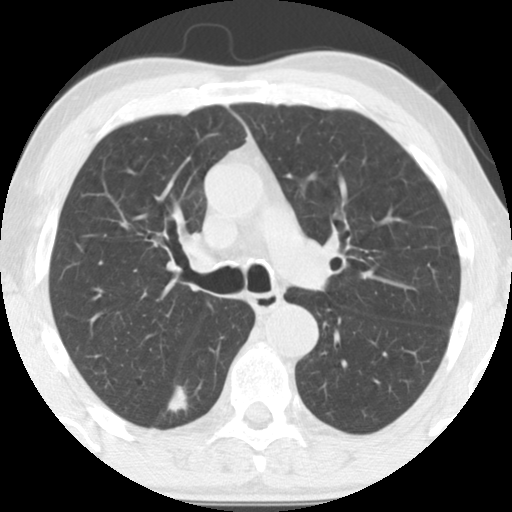
Low-dose screening chest CT, one axial slice; slice 92 of 135 in the series (ordered by position); reconstruction kernel STANDARD; 120 kVp; lung window (W 1500 / L -600 HU); 2.5 mm slice thickness; 512 × 512 image matrix.
Outlined on this slice (expert manual segmentation):
- lesion 1 (tumor, lower lobe of right lung): box from (x=168, y=386) to (x=187, y=412) px